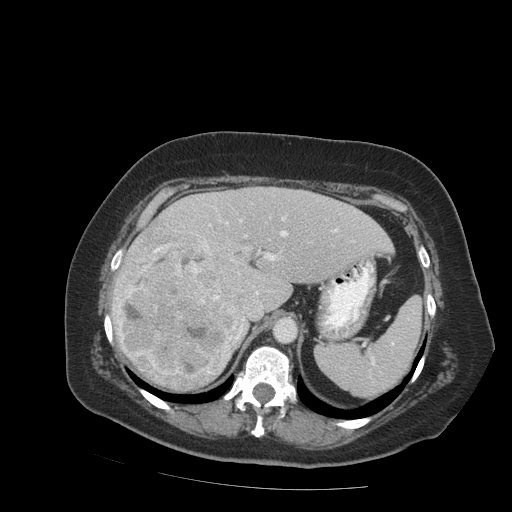
Contrast-enhanced abdominal CT (liver protocol), one axial slice. Position 58 of 99 along the scan axis. Reconstruction kernel STANDARD. Soft-tissue window (W 400 / L 40 HU). 2.5 mm slice thickness. 512 × 512 image matrix. From the clinical record (not read from this slice): diagnosis: hepatocellular carcinoma (patient treated with transarterial chemoembolisation; whether this scan precedes or follows treatment is not stated here); TNM stage (as recorded): Stage-IVB; Child-Pugh class: A; tumour differentiation: moderately differentiated; tumour nodularity: uninodular.
Outlined on this slice (semi-automatically segmented with operator editing):
- liver parenchyma outside the tumour (the mass and vessels are separate outlines, so this box may not span the whole liver): bounding box [x1, y1, x2, y2] px = [112, 186, 392, 390]
- mass: [115, 226, 245, 388]
- liver vessels: [201, 217, 337, 294]